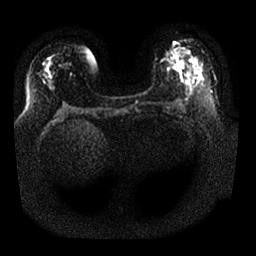
Breast MRI, one axial slice; position 9 of 25 along the scan axis; diffusion-weighted series; image 2 of 4 stored at this slice position (different b-values; order by instance number); 1.5 T; 256 × 256 image matrix, field of view 350 × 350 mm. Female patient.
Structures marked on this image (outlined manually by an expert reader):
- tumour on diffusion-weighted imaging: box from (x=175, y=62) to (x=185, y=71) px